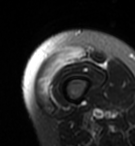
MRI of an extremity soft-tissue mass, one axial slice. Position 7 of 95 along the scan axis. T2-weighted fat-saturated. MR volume resampled by the dataset authors to the PET/CT grid (not the native acquisition matrix). 3.27 mm slice thickness. 135 × 146 image matrix, field of view 132 × 143 mm. Female patient. From the clinical record (not read from this slice): histological type: pleiomorphic undifferentiated sarcoma; grade: high; site of the primary tumour: right quadricep.
Outlined on this slice (expert contour drawn on MRI and transferred to this co-registered scan by the dataset authors):
- gross tumour volume including surrounding oedema: bounding box [x1, y1, x2, y2] px = [39, 47, 86, 98]